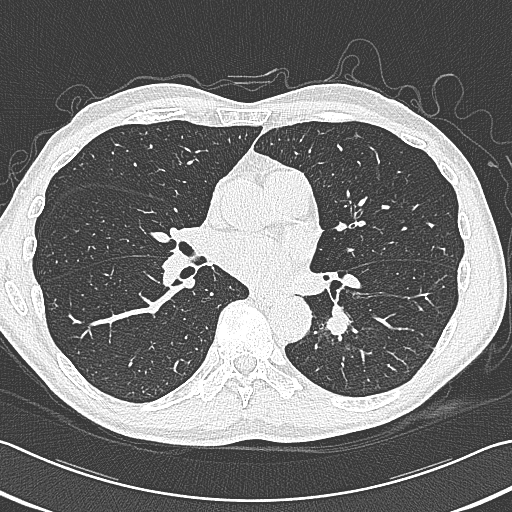
Chest CT (low-dose screening protocol), one axial image, baseline annual screen, lung window (W 1500 / L -600 HU), 120 kVp. Male participant, aged 59 years at enrolment. Former smoker at enrolment.
- Expert reader's lesion annotation, box from (x=312, y=296) to (x=376, y=353) px.
- Screening reader's record for this exam (one nodule recorded; not confirmed to be the boxed lesion): non-calcified nodule or mass ≥4 mm, left lower lobe, 15 × 15 mm, smooth margins, soft tissue attenuation.
- Participant outcome: lung cancer diagnosed 17 days after this screen — squamous cell carcinoma, large cell, nonkeratinizing, NOS, left lower lobe, poorly differentiated (G3), stage IB (AJCC 6th edition), 31 mm at pathology.